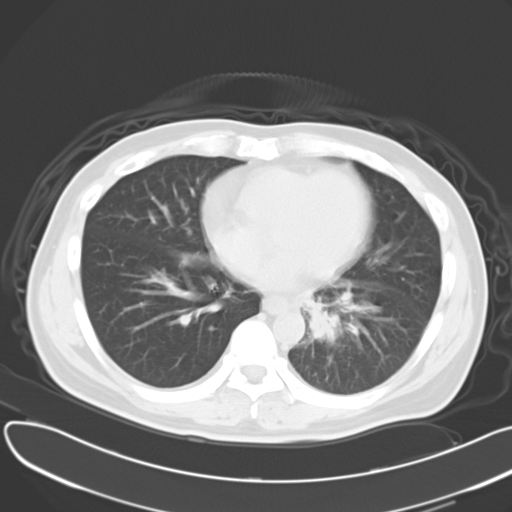
Chest CT, one axial slice; position 13 of 30 along the scan axis; 120 kVp; lung window (W 1500 / L -600 HU); 10 mm slice thickness; 512 × 512 image matrix. Patient: male, 55 years. Case-level facts recorded for this patient, not image findings: clinical TNM (as recorded): T2 N3 M0.
Structures marked on this image (bounding box drawn by a radiologist):
- lung tumour (recorded histology: small cell carcinoma): bounding box [x1, y1, x2, y2] px = [305, 288, 341, 349]